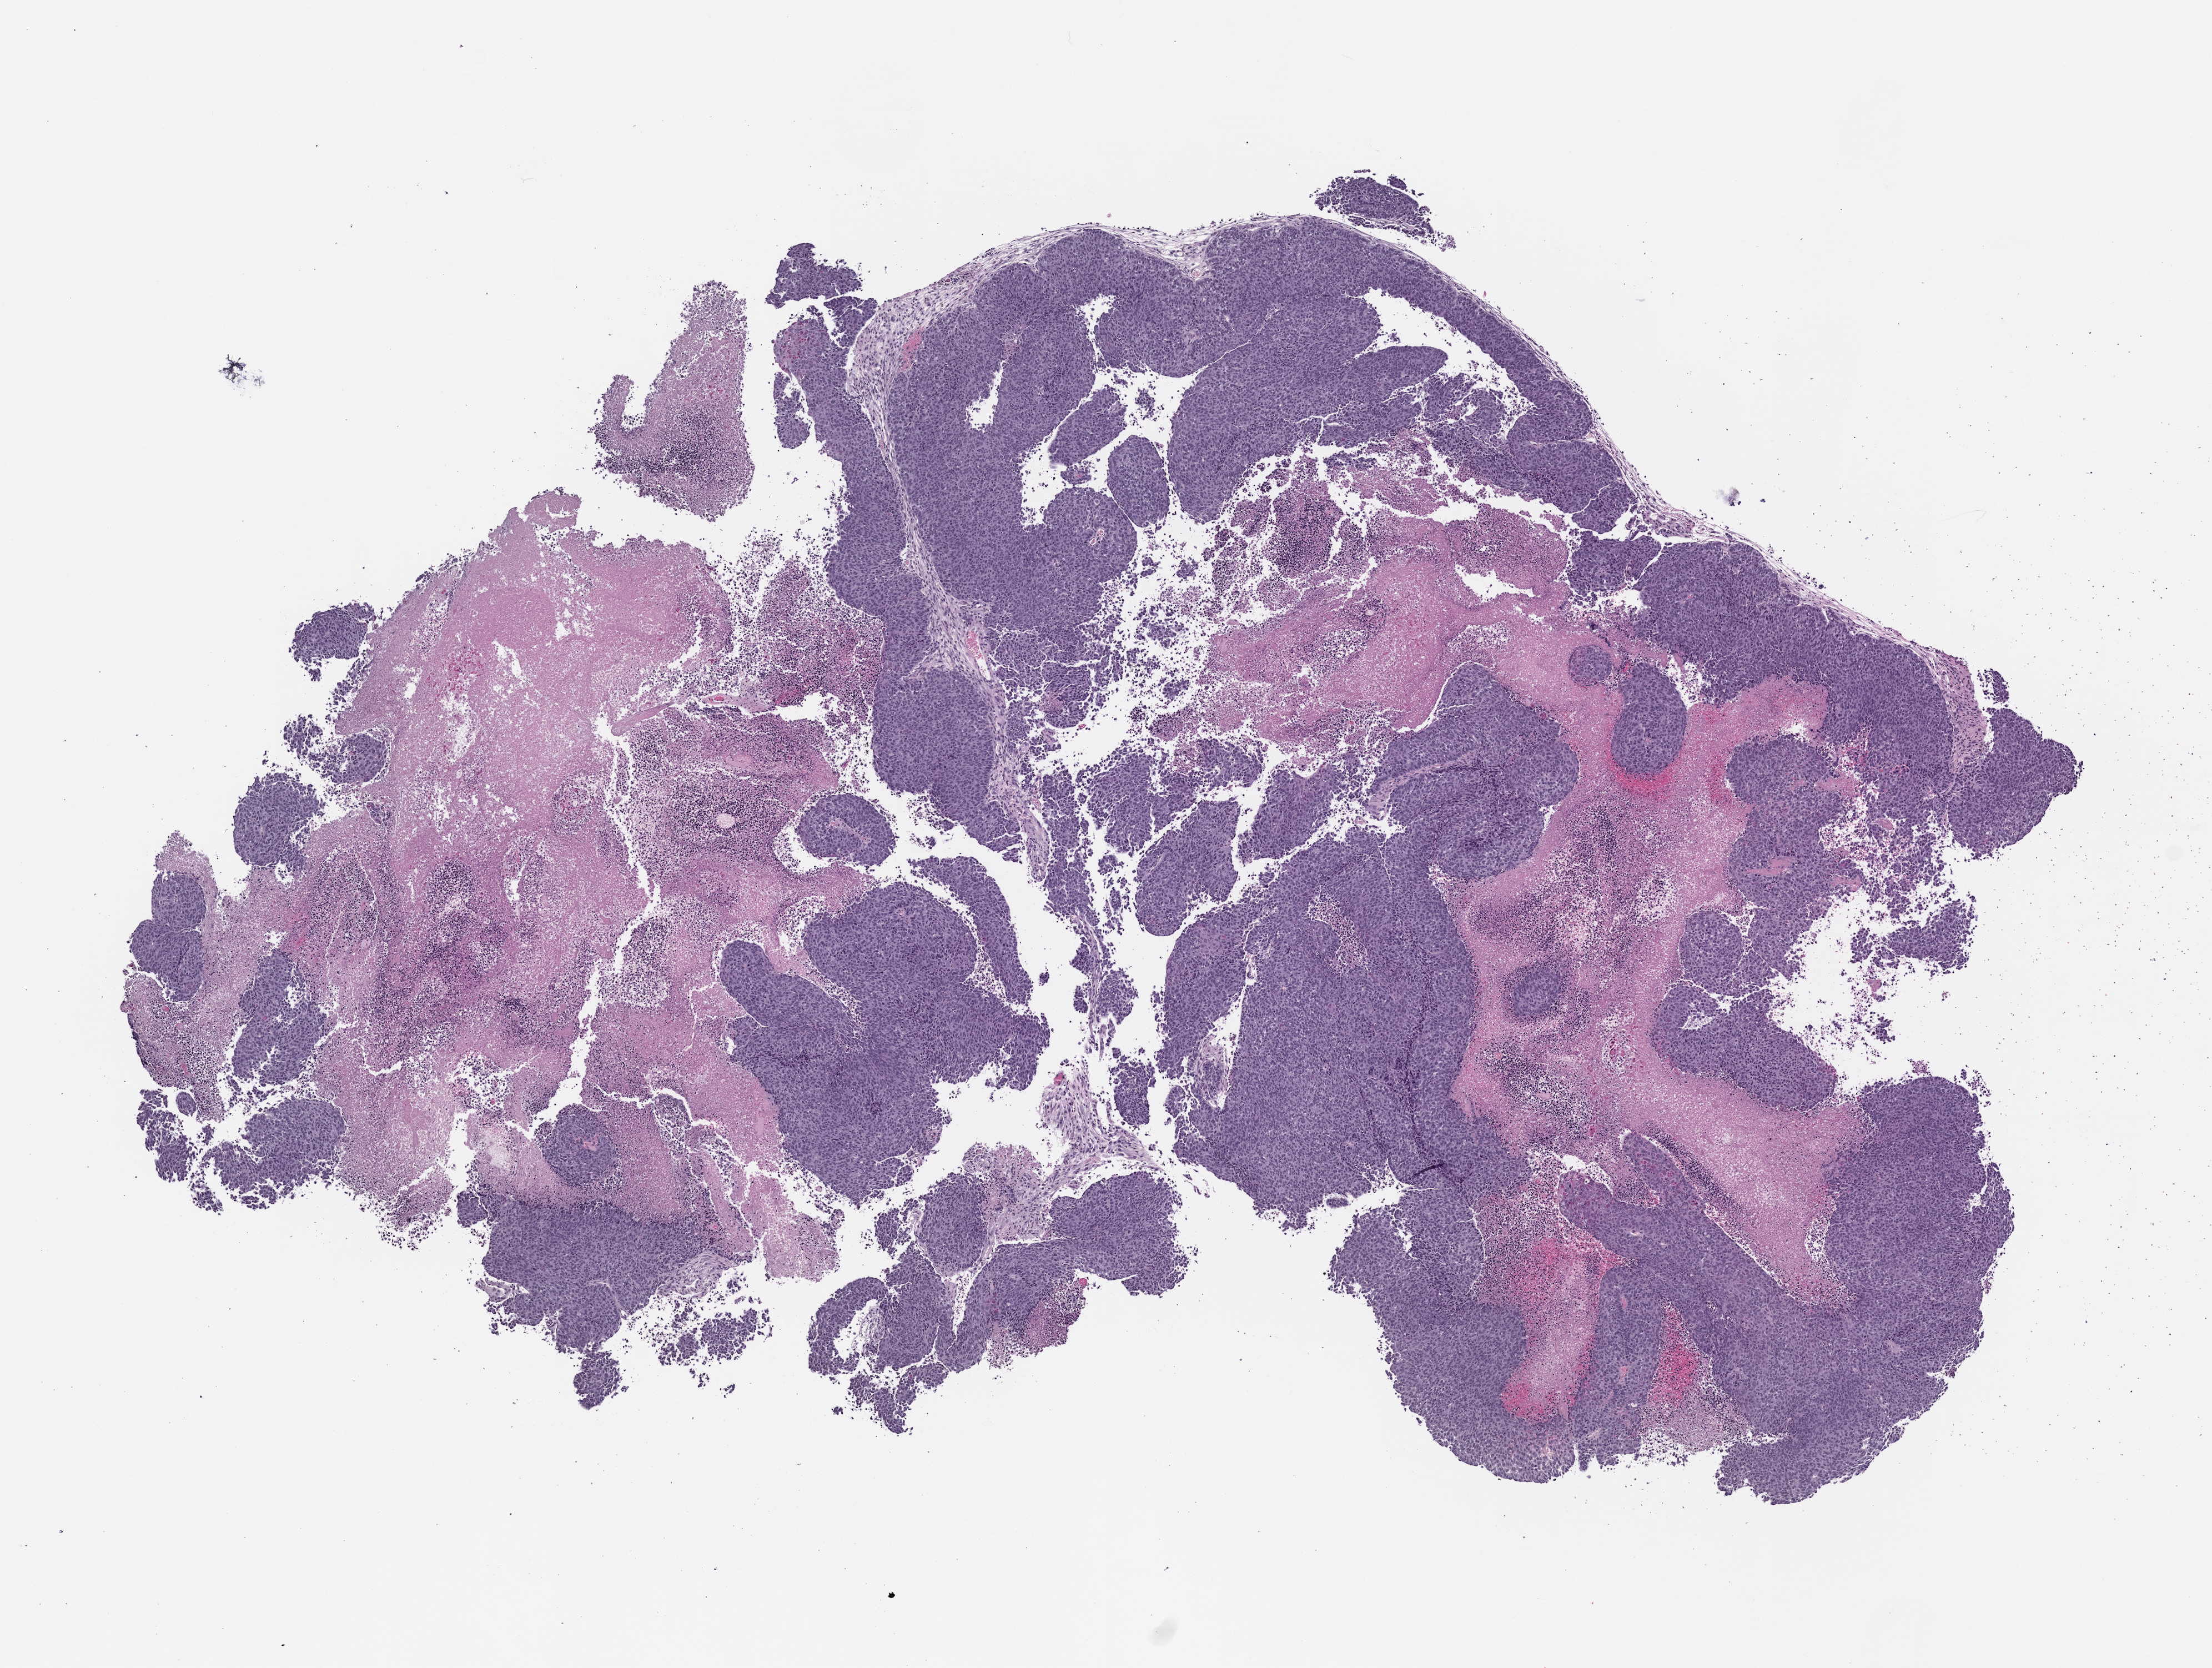
Whole-slide image, H&E: patient-derived xenograft (human tumor grown in a mouse), passage 1 — whole scanned area (about 8.0 x 6.0 mm) shown as a low-resolution overview, FFPE section, originating tumor site category: vagina.
Originating patient diagnosis: Vaginal Carcinoma.